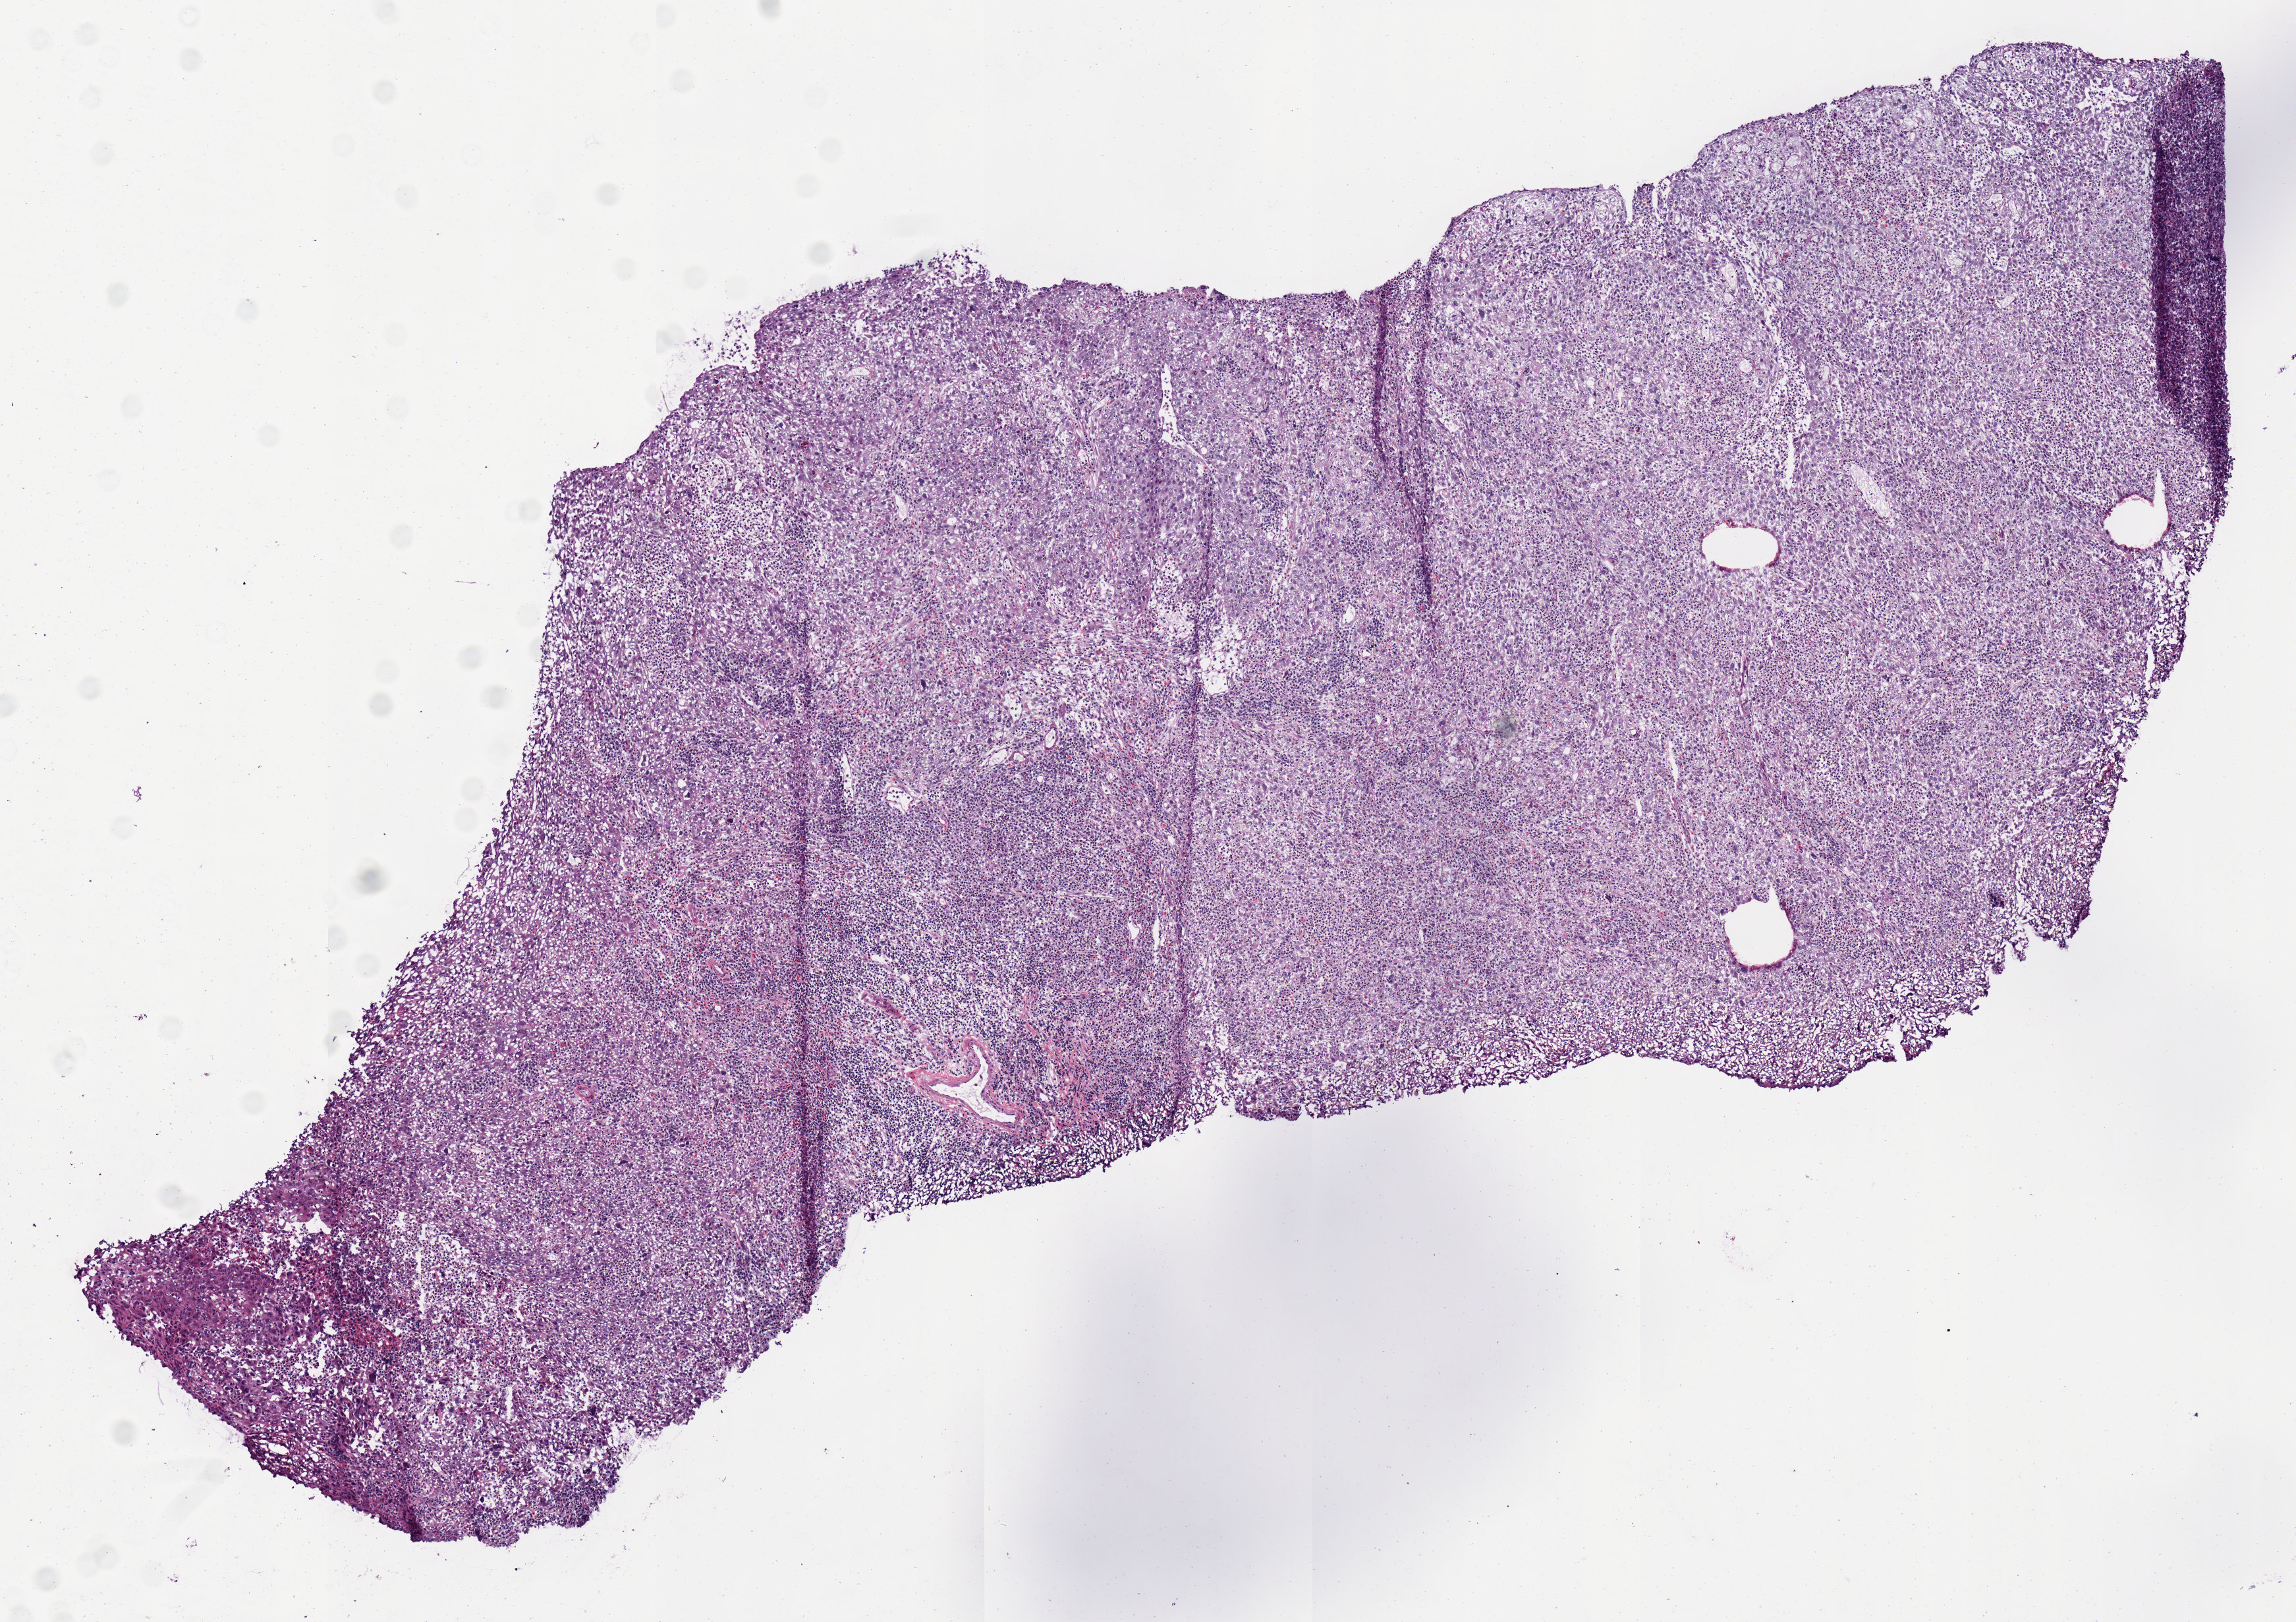
Digitized Hematoxylin and eosin (H&E) stained tissue section (whole slide) — low-resolution overview of the scanned area, about 6.9 x 4.9 mm; frozen section from the top of the tissue portion; primary tumour sample from the cervix. Patient: female, age at initial diagnosis 32 years. Histologic grade: G3 (poorly differentiated). Pathologist review of this section (percent, as recorded): tumour cells 95%, tumour nuclei 60%, normal cells 0%, stromal cells 5%, necrosis 0%. Inflammatory infiltration, as recorded: lymphocyte infiltration 0%, monocyte infiltration 0%, neutrophil infiltration 0%.
- histologic diagnosis: Squamous cell carcinoma, NOS (cervix uteri)
- FIGO stage: IIA1